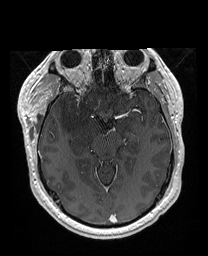
Brain MRI from a brain-tumour surgery series, one axial slice. Position 110 of 176 along the scan axis. T1-weighted post-contrast. 1 mm slice thickness. 208 × 256 image matrix, field of view 208 × 256 mm. Case-level facts recorded for this patient, not image findings: histopathology: Astrocytoma; WHO grade: 4; IDH mutation: yes; tumour location: Right Orbitofrontal Anterior Temporal Insular.
Annotated regions visible in this slice (manually delineated by an expert):
- previous resection cavity: bounding box <64,63,71,71> (left, top, right, bottom; pixels)